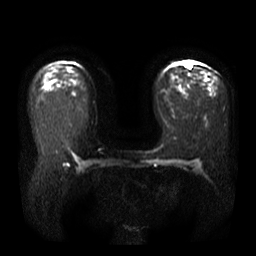
Breast MRI, one axial slice; position 23 of 40 along the scan axis; diffusion-weighted series; image 2 of 4 stored at this slice position (different b-values; order by instance number); 3 T; 5 mm slice thickness; 256 × 256 image matrix. Female patient.
Structures marked on this image (manually delineated by an expert):
- tumour on diffusion-weighted imaging: box from (x=186, y=64) to (x=192, y=68) px